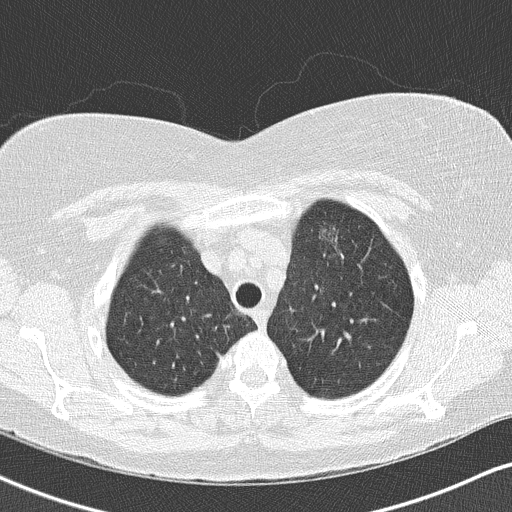
Low-dose screening chest CT, one axial slice; position 118 of 146 along the scan axis; 120 kVp; lung window (W 1500 / L -600 HU); 2 mm slice thickness; 512 × 512 image matrix, field of view 328 × 328 mm.
Annotated regions visible in this slice (outlined manually by an expert reader):
- lesion 1 (tumor, upper lobe of left lung): bounding box [x1, y1, x2, y2] px = [319, 227, 339, 248]